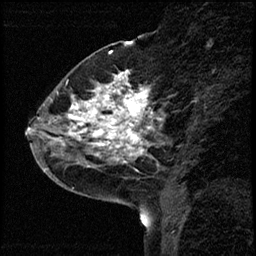
Breast MRI (dynamic contrast-enhanced), one sagittal slice. Position 21 of 68 along the scan axis. Dynamic contrast-enhanced study with each time point stored as its own series, time point 2 of 3 at this slice position (early post-contrast, ordered by acquisition time). 1.5 T. TE 4.2 ms, TR 17.6 ms. 256 × 256 image matrix. Female patient, age 52 years. Case-level facts recorded for this patient, not image findings: setting: breast cancer imaged before/during neoadjuvant chemotherapy; receptor status: HER2-positive.
Structures marked on this image (semi-automatically segmented with operator editing):
- analysis volume of interest (the breast-tissue region the enhancement analysis was run in; not a lesion): bounding box [x1, y1, x2, y2] px = [50, 61, 163, 184]
- tumour enhancement mask (voxels above the 100 % enhancement threshold inside the analysis volume of interest): [50, 73, 157, 163]